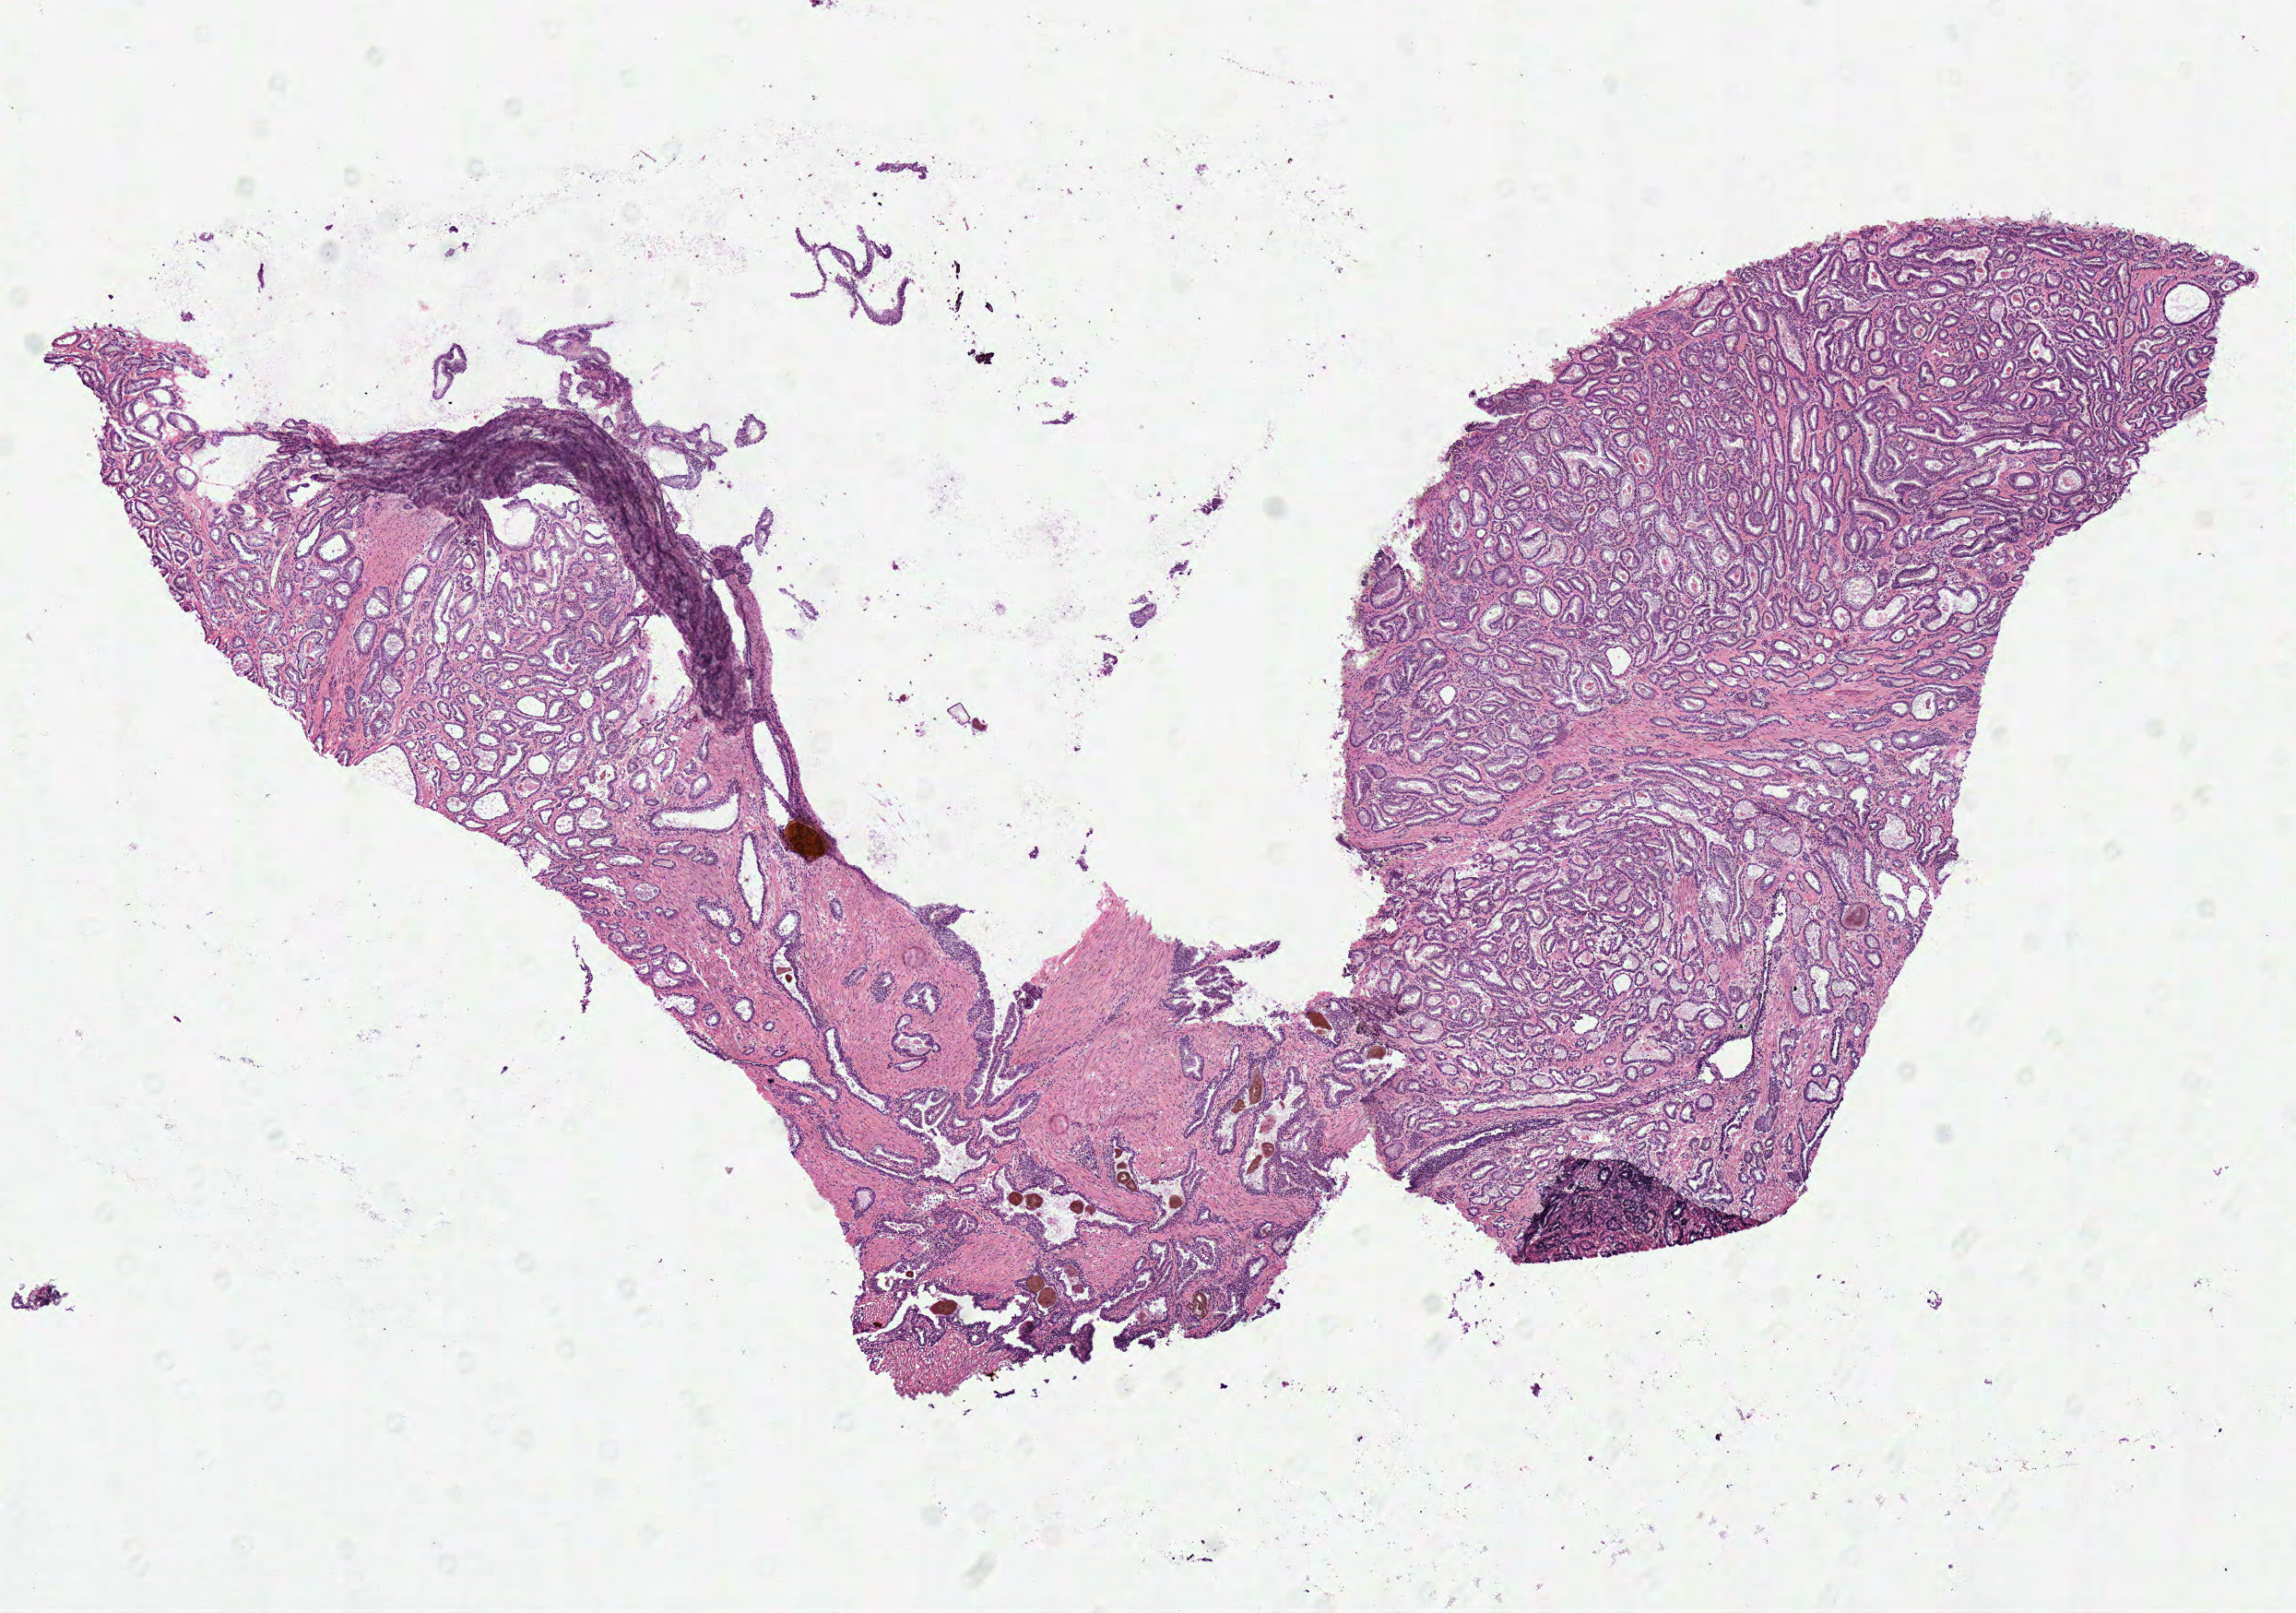
Digitized H&E-stained tissue section (whole slide), shown as a low-resolution overview of the whole scanned area (about 9.8 x 6.9 mm); frozen section from the top of the tissue portion; prostate, primary tumour sample. Male, age 52 years at initial diagnosis. Gleason score: 7 (3+4). Pathologist review of this section (percent, as recorded): tumour cells 70%, tumour nuclei 75%, normal cells 15%, stromal cells 15%, necrosis 0%. Infiltration values recorded for this section: lymphocyte infiltration 2%, monocyte infiltration 0%, neutrophil infiltration 0%.
* histologic diagnosis: Acinar cell carcinoma (prostate gland)
* lymph nodes positive (case pathology): 0 of 1 examined